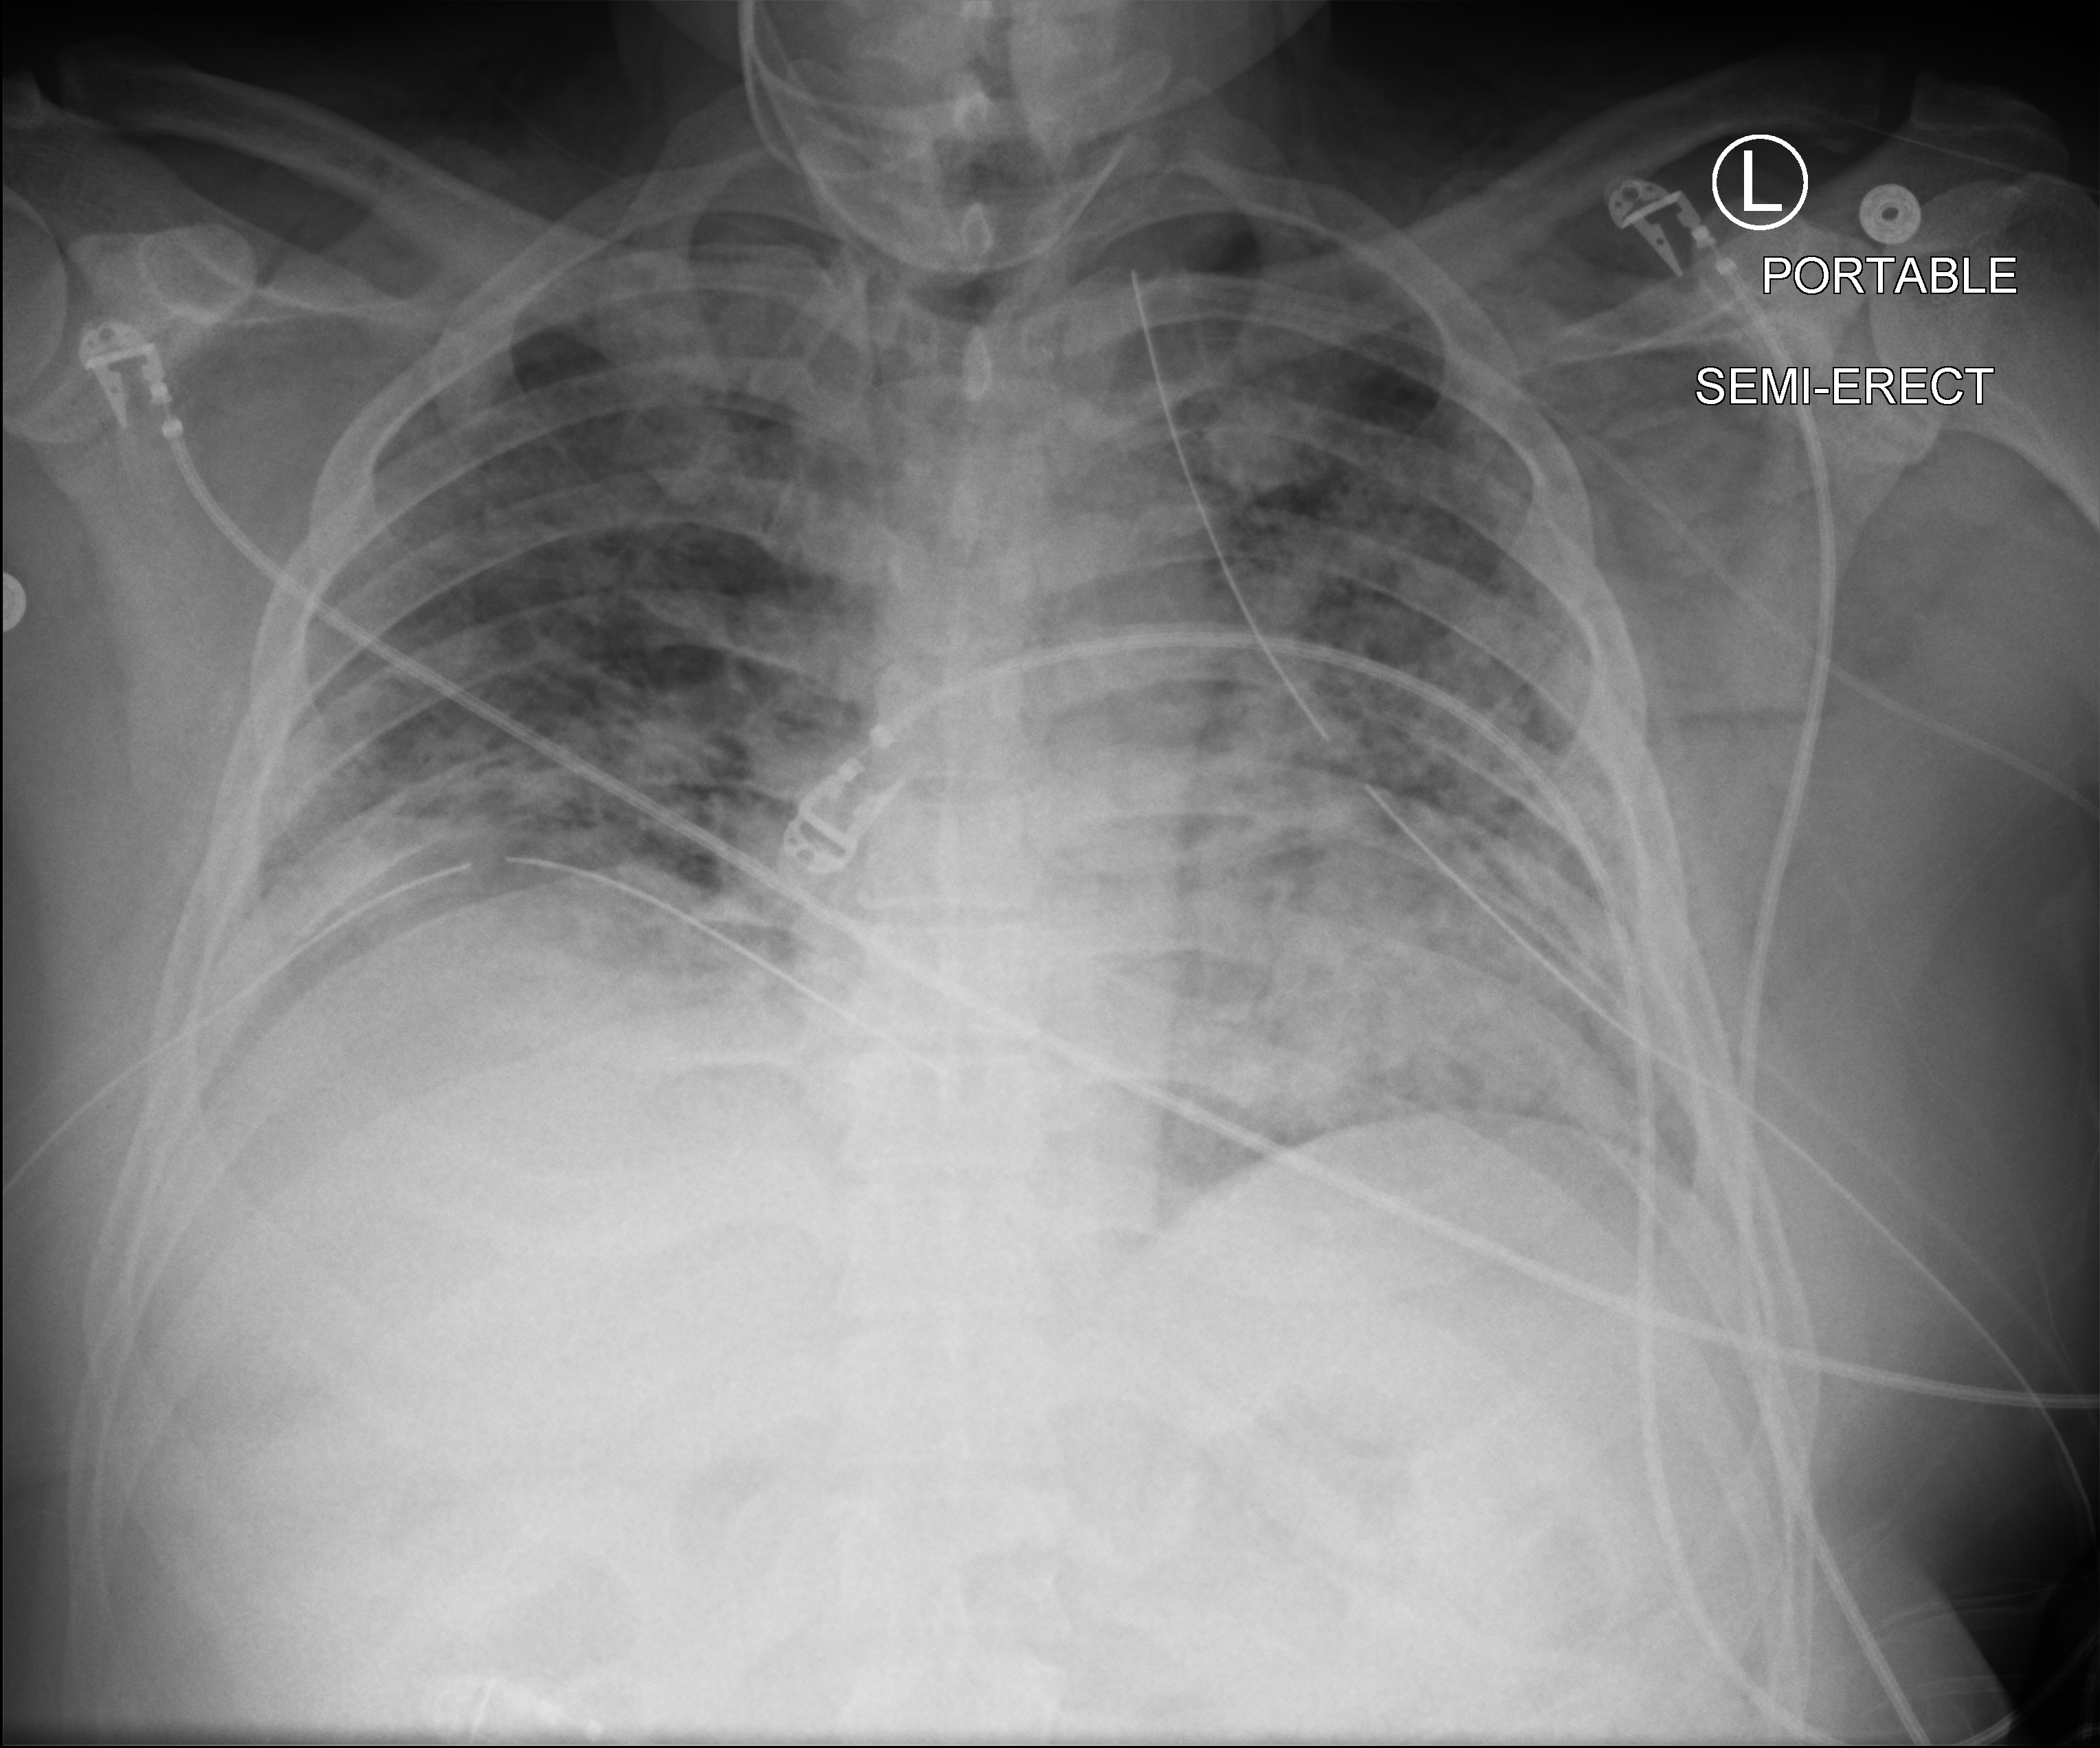
Bedside chest radiograph (computed radiography). Male patient hospitalised with COVID-19, age 18–59 years.
From the hospital-stay record, not from the radiograph (when in the stay this image was taken is not recorded):
- mechanically ventilated during this hospital stay: yes
- admitted to intensive care during this hospital stay: yes